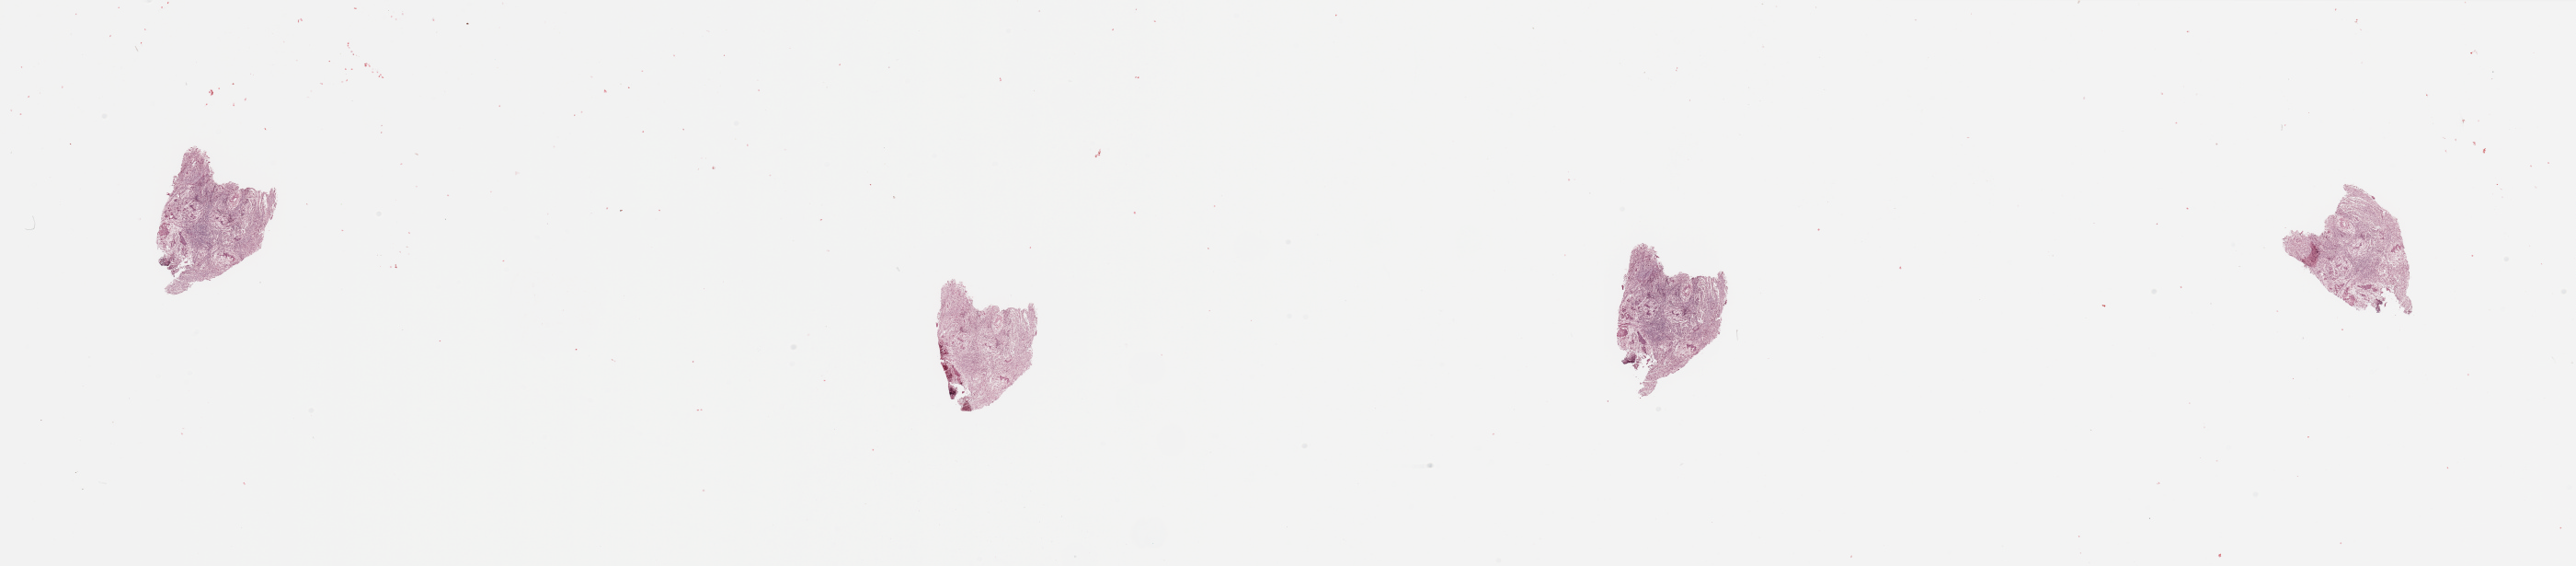
Digitized H&E-stained tissue section (whole slide), whole scanned area (about 44.3 x 9.7 mm) shown as a low-resolution overview. Uterus, tumour tissue. Female, 80 y/o. Histologic grade: G2 (moderately differentiated).
- AJCC pathologic stage: I
- histologic diagnosis: Endometrioid adenocarcinoma, NOS
- primary tumour site (as recorded): anterior endometrium